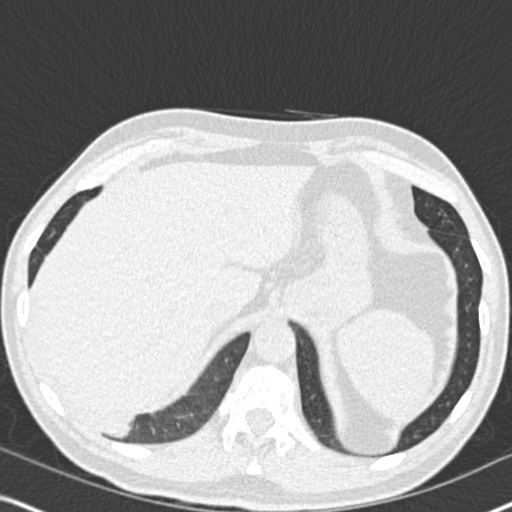
Low-dose screening chest CT, one axial slice. Position 44 of 182 along the scan axis. Lung window (W 1500 / L -600 HU). 2 mm slice thickness. 512 × 512 image matrix.
Outlined on this slice (manually delineated by an expert):
- lesion 1 (tumor, lower lobe of right lung): bounding box [x1, y1, x2, y2] px = [81, 412, 133, 435]